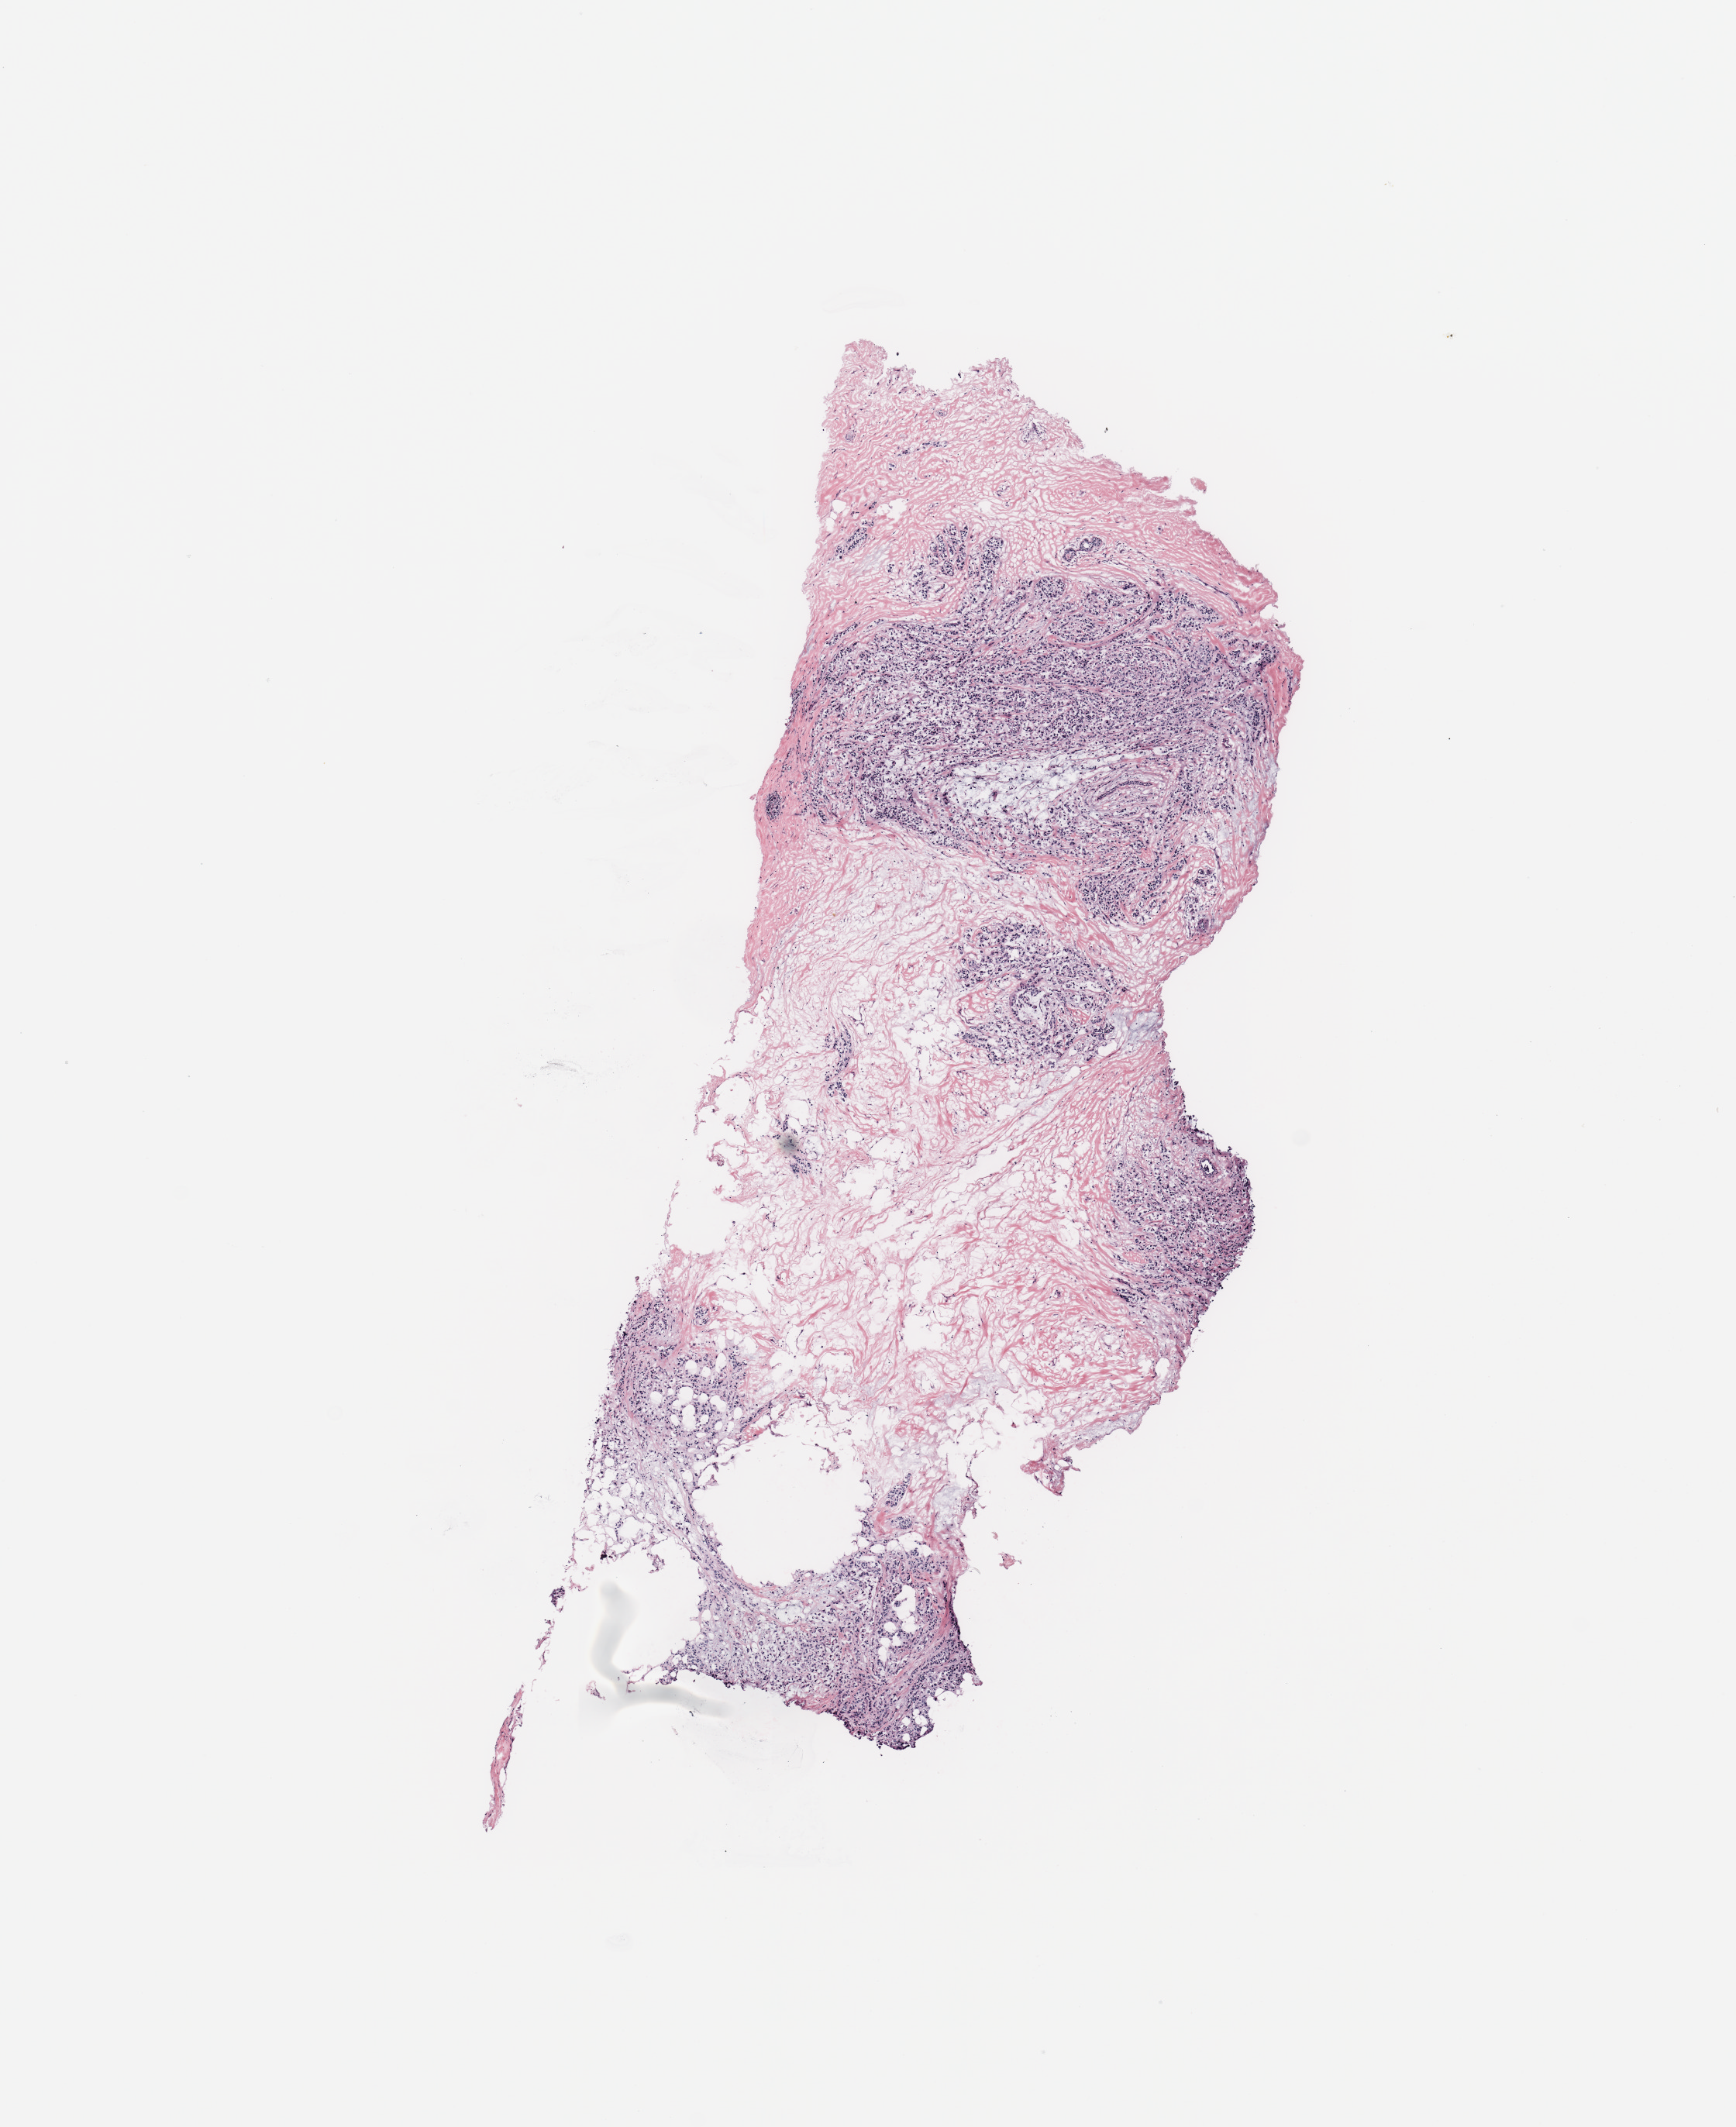
Digitized H&E tissue section (whole slide), a low-resolution overview of the entire scanned area, about 8.9 x 10.9 mm (acquisition: 20x scan); tumour tissue sample, breast. Female, 71 y/o.
* AJCC pathologic stage: IIIA
* histologic diagnosis: Invasive lobular carcinoma